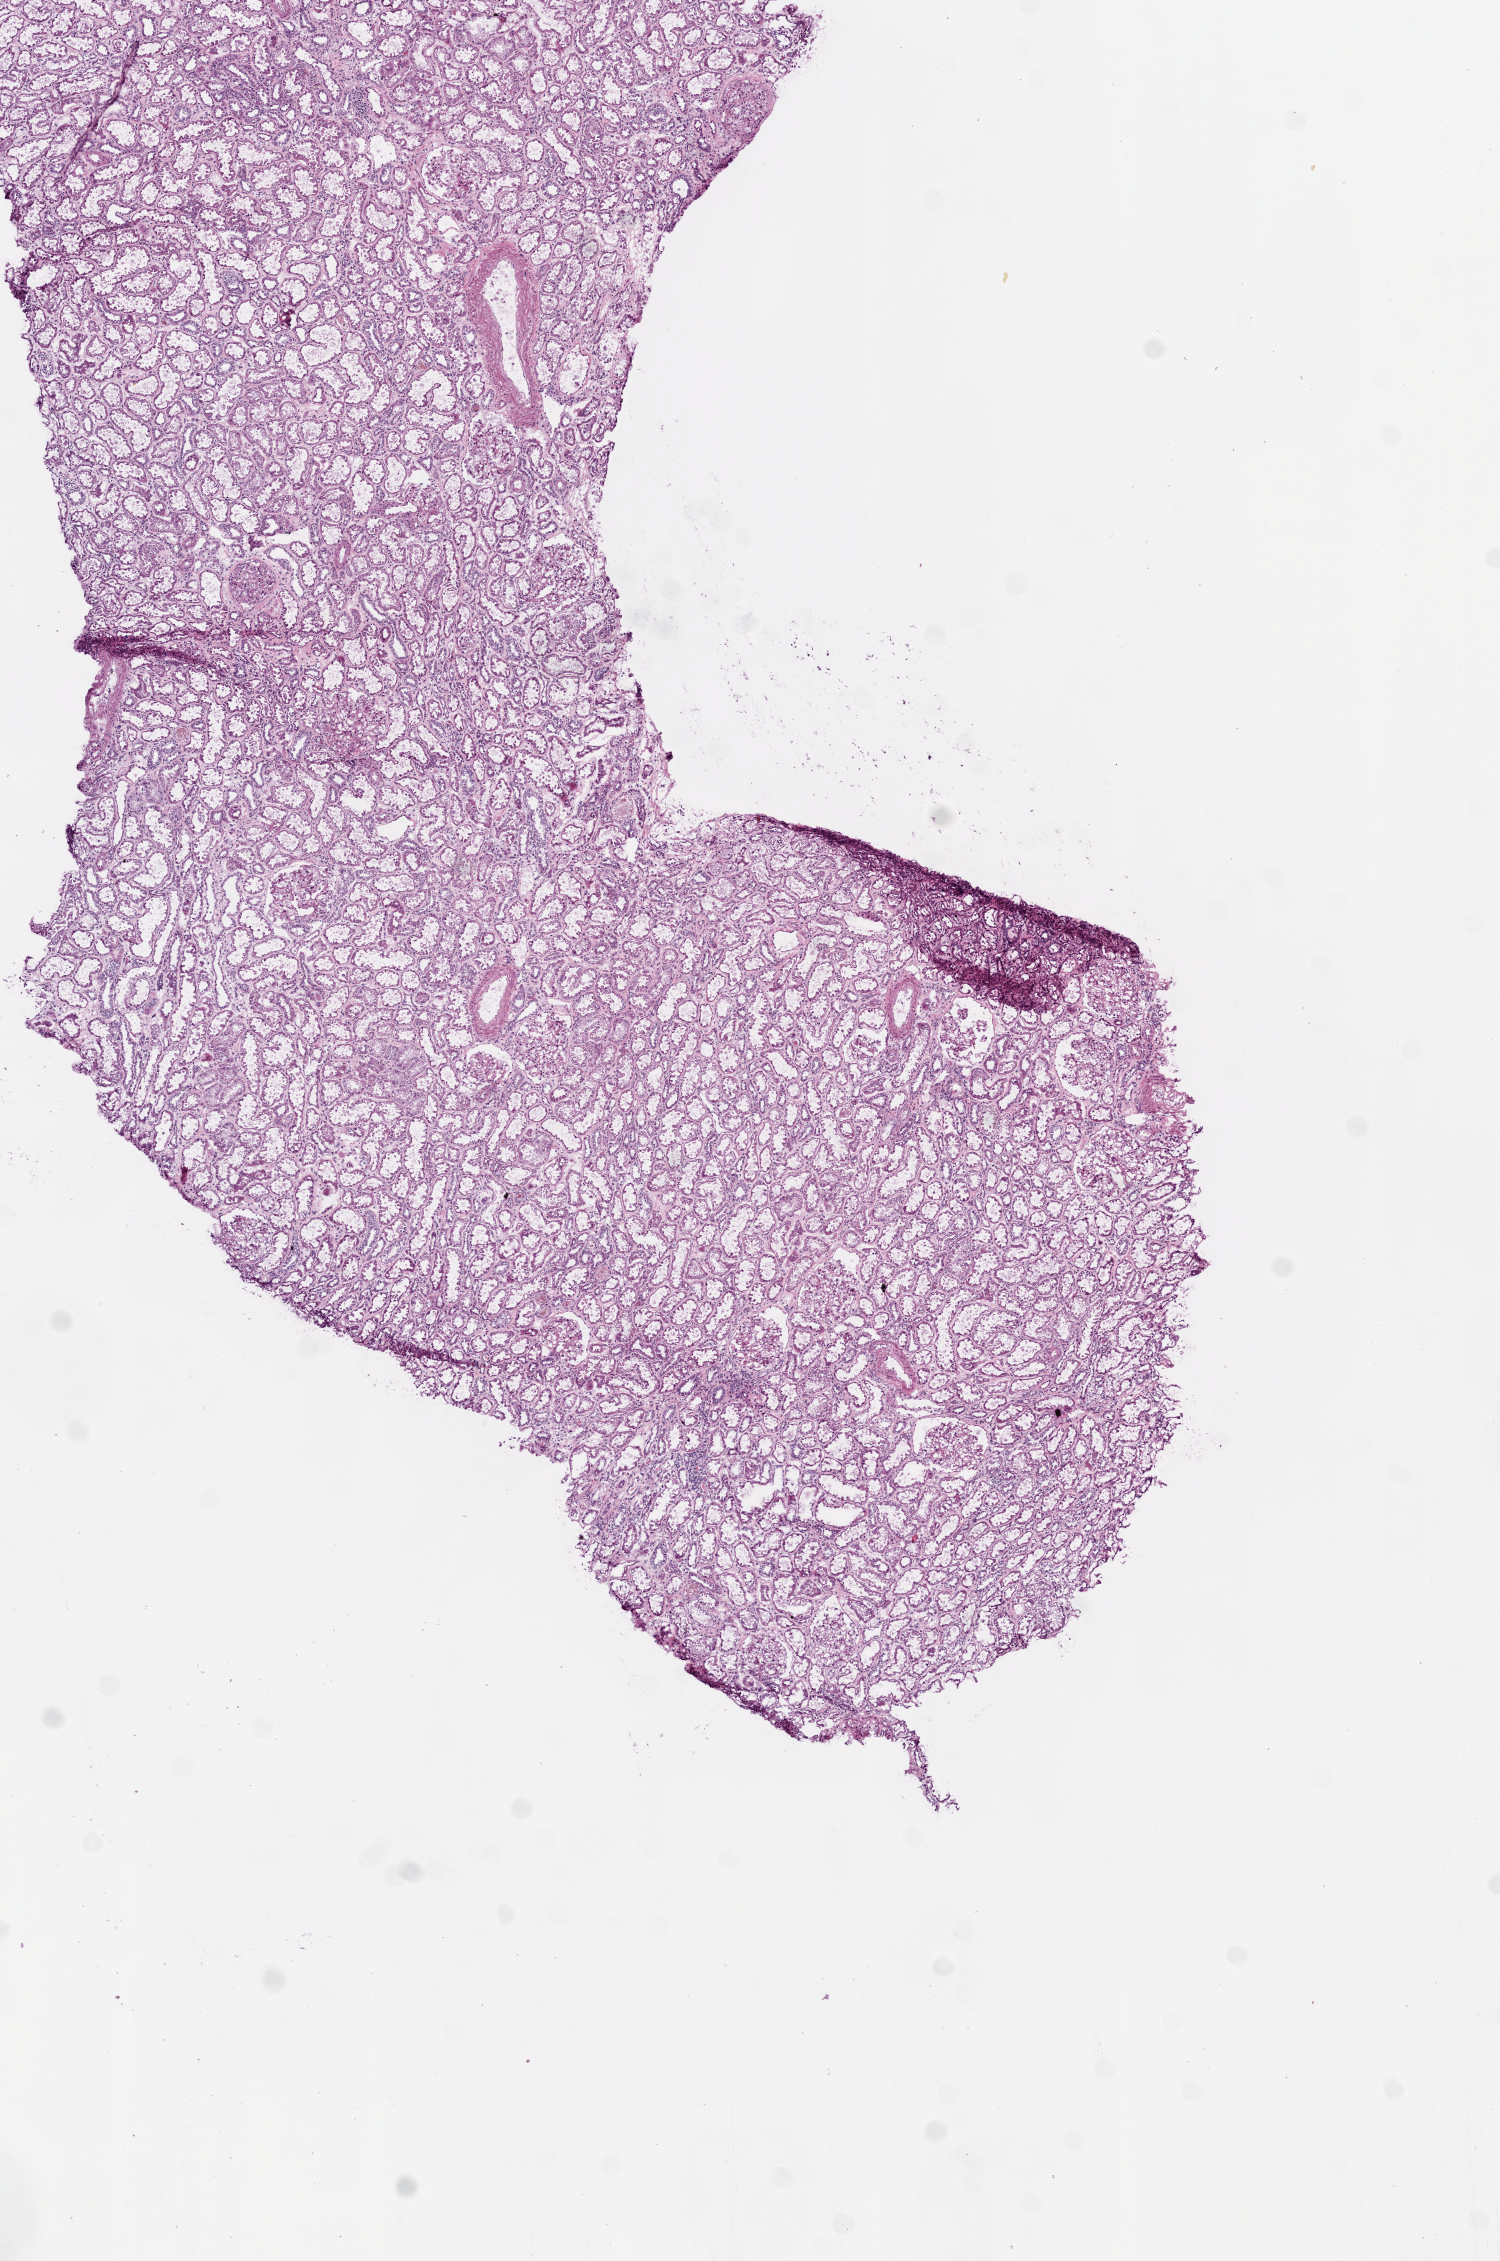
Digitized H&E tissue section (whole slide) — a low-resolution overview of the entire scanned area, about 6.0 x 9.1 mm (acquisition: 20x scan), frozen section from the top of the tissue portion, solid tissue normal (non-tumour tissue) sample from the kidney. Male patient; age at initial diagnosis 58 years.
This section: solid tissue normal (non-tumour) sample from the same patient. Patient diagnosis: Clear cell adenocarcinoma, NOS.